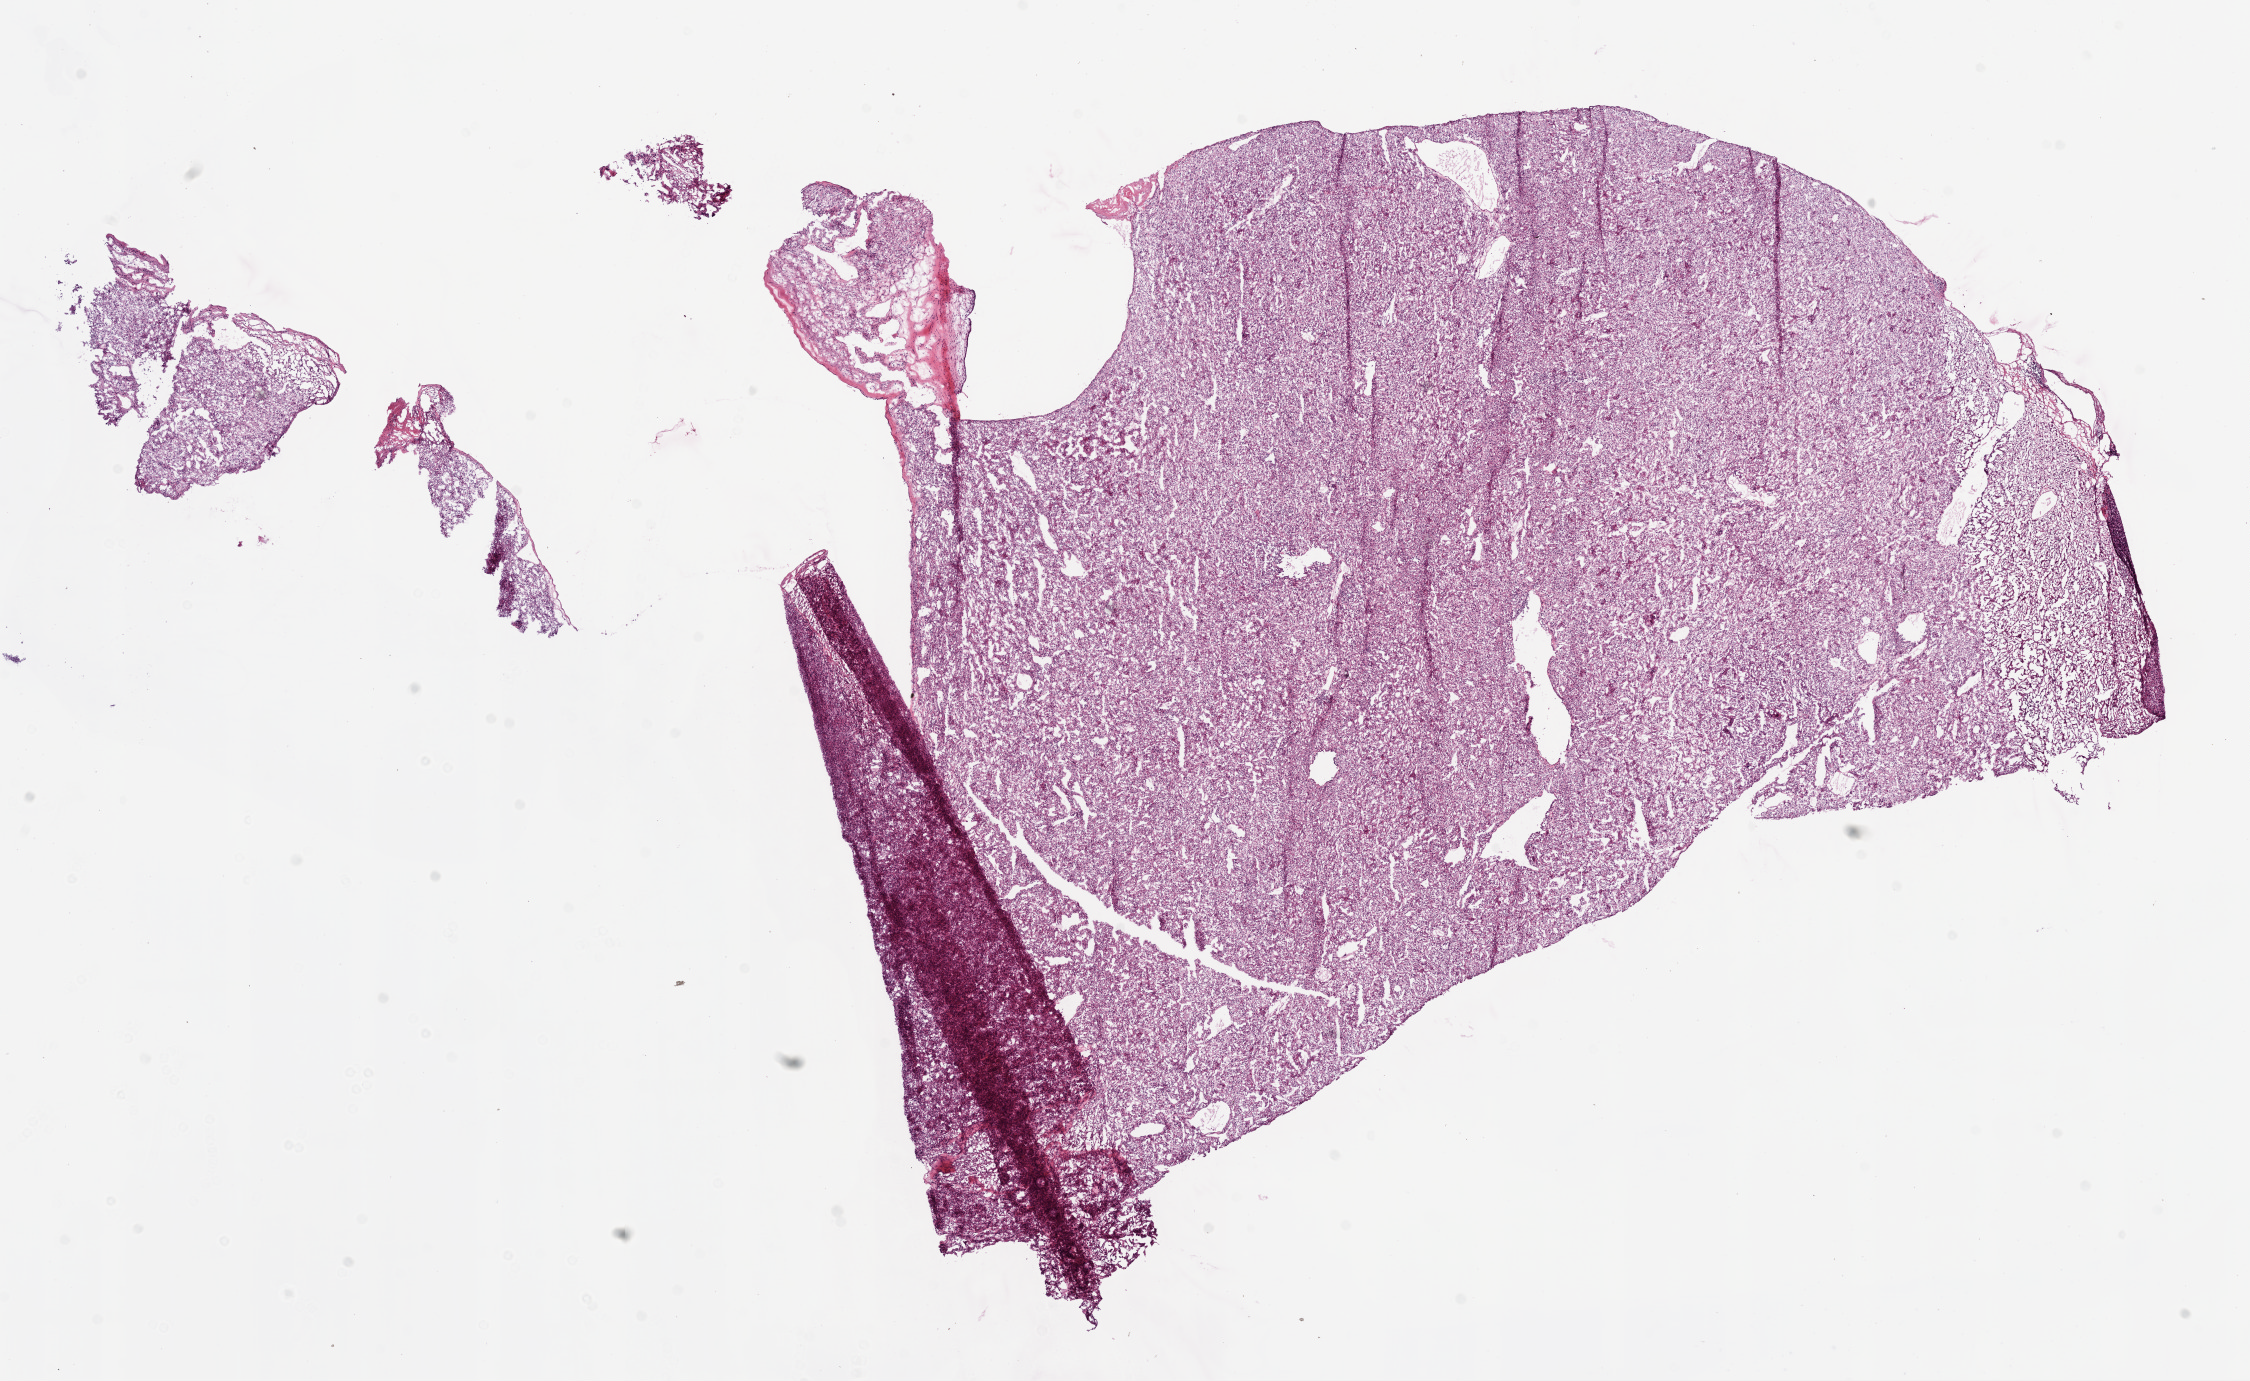
Digitized H&E-stained tissue section (whole slide) — low-resolution overview of the scanned area, about 18.1 x 11.1 mm (slide scanned at 20x); frozen section from the bottom of the tissue portion; kidney, primary tumour sample. Male patient; age at initial diagnosis 82 years. Histologic grade: G2 (moderately differentiated). Pathologist review of this section (percent, as recorded): tumour cells 95%, tumour nuclei 90%, normal cells 0%, stromal cells 5%, necrosis 0%.
Histologic diagnosis: Clear cell adenocarcinoma, NOS. AJCC pathologic stage: I. TNM: T1a NX M0.